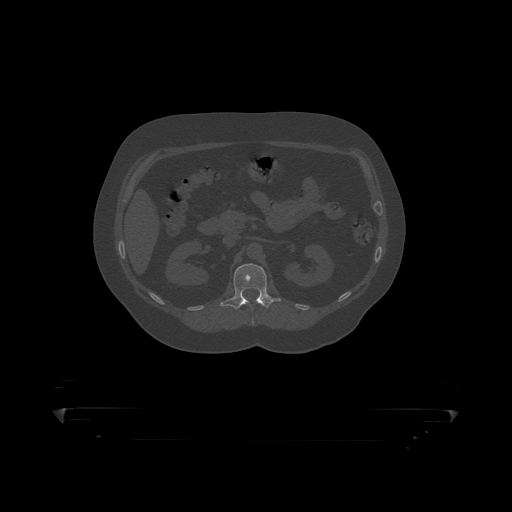
CT including the spine, one axial slice. Position 150 of 390 along the scan axis. 120 kVp. Bone window (W 1800 / L 400 HU). 1.25 mm slice thickness. 512 × 512 image matrix. Patient: male, 60 years. From the clinical record (not read from this slice): primary cancer: prostate.
Annotated regions visible in this slice (semi-automatic segmentation, software-assisted and operator-edited):
- L1 vertebra: bounding box <221,264,281,311> (left, top, right, bottom; pixels)
- T12 vertebra: <259,302,263,307>